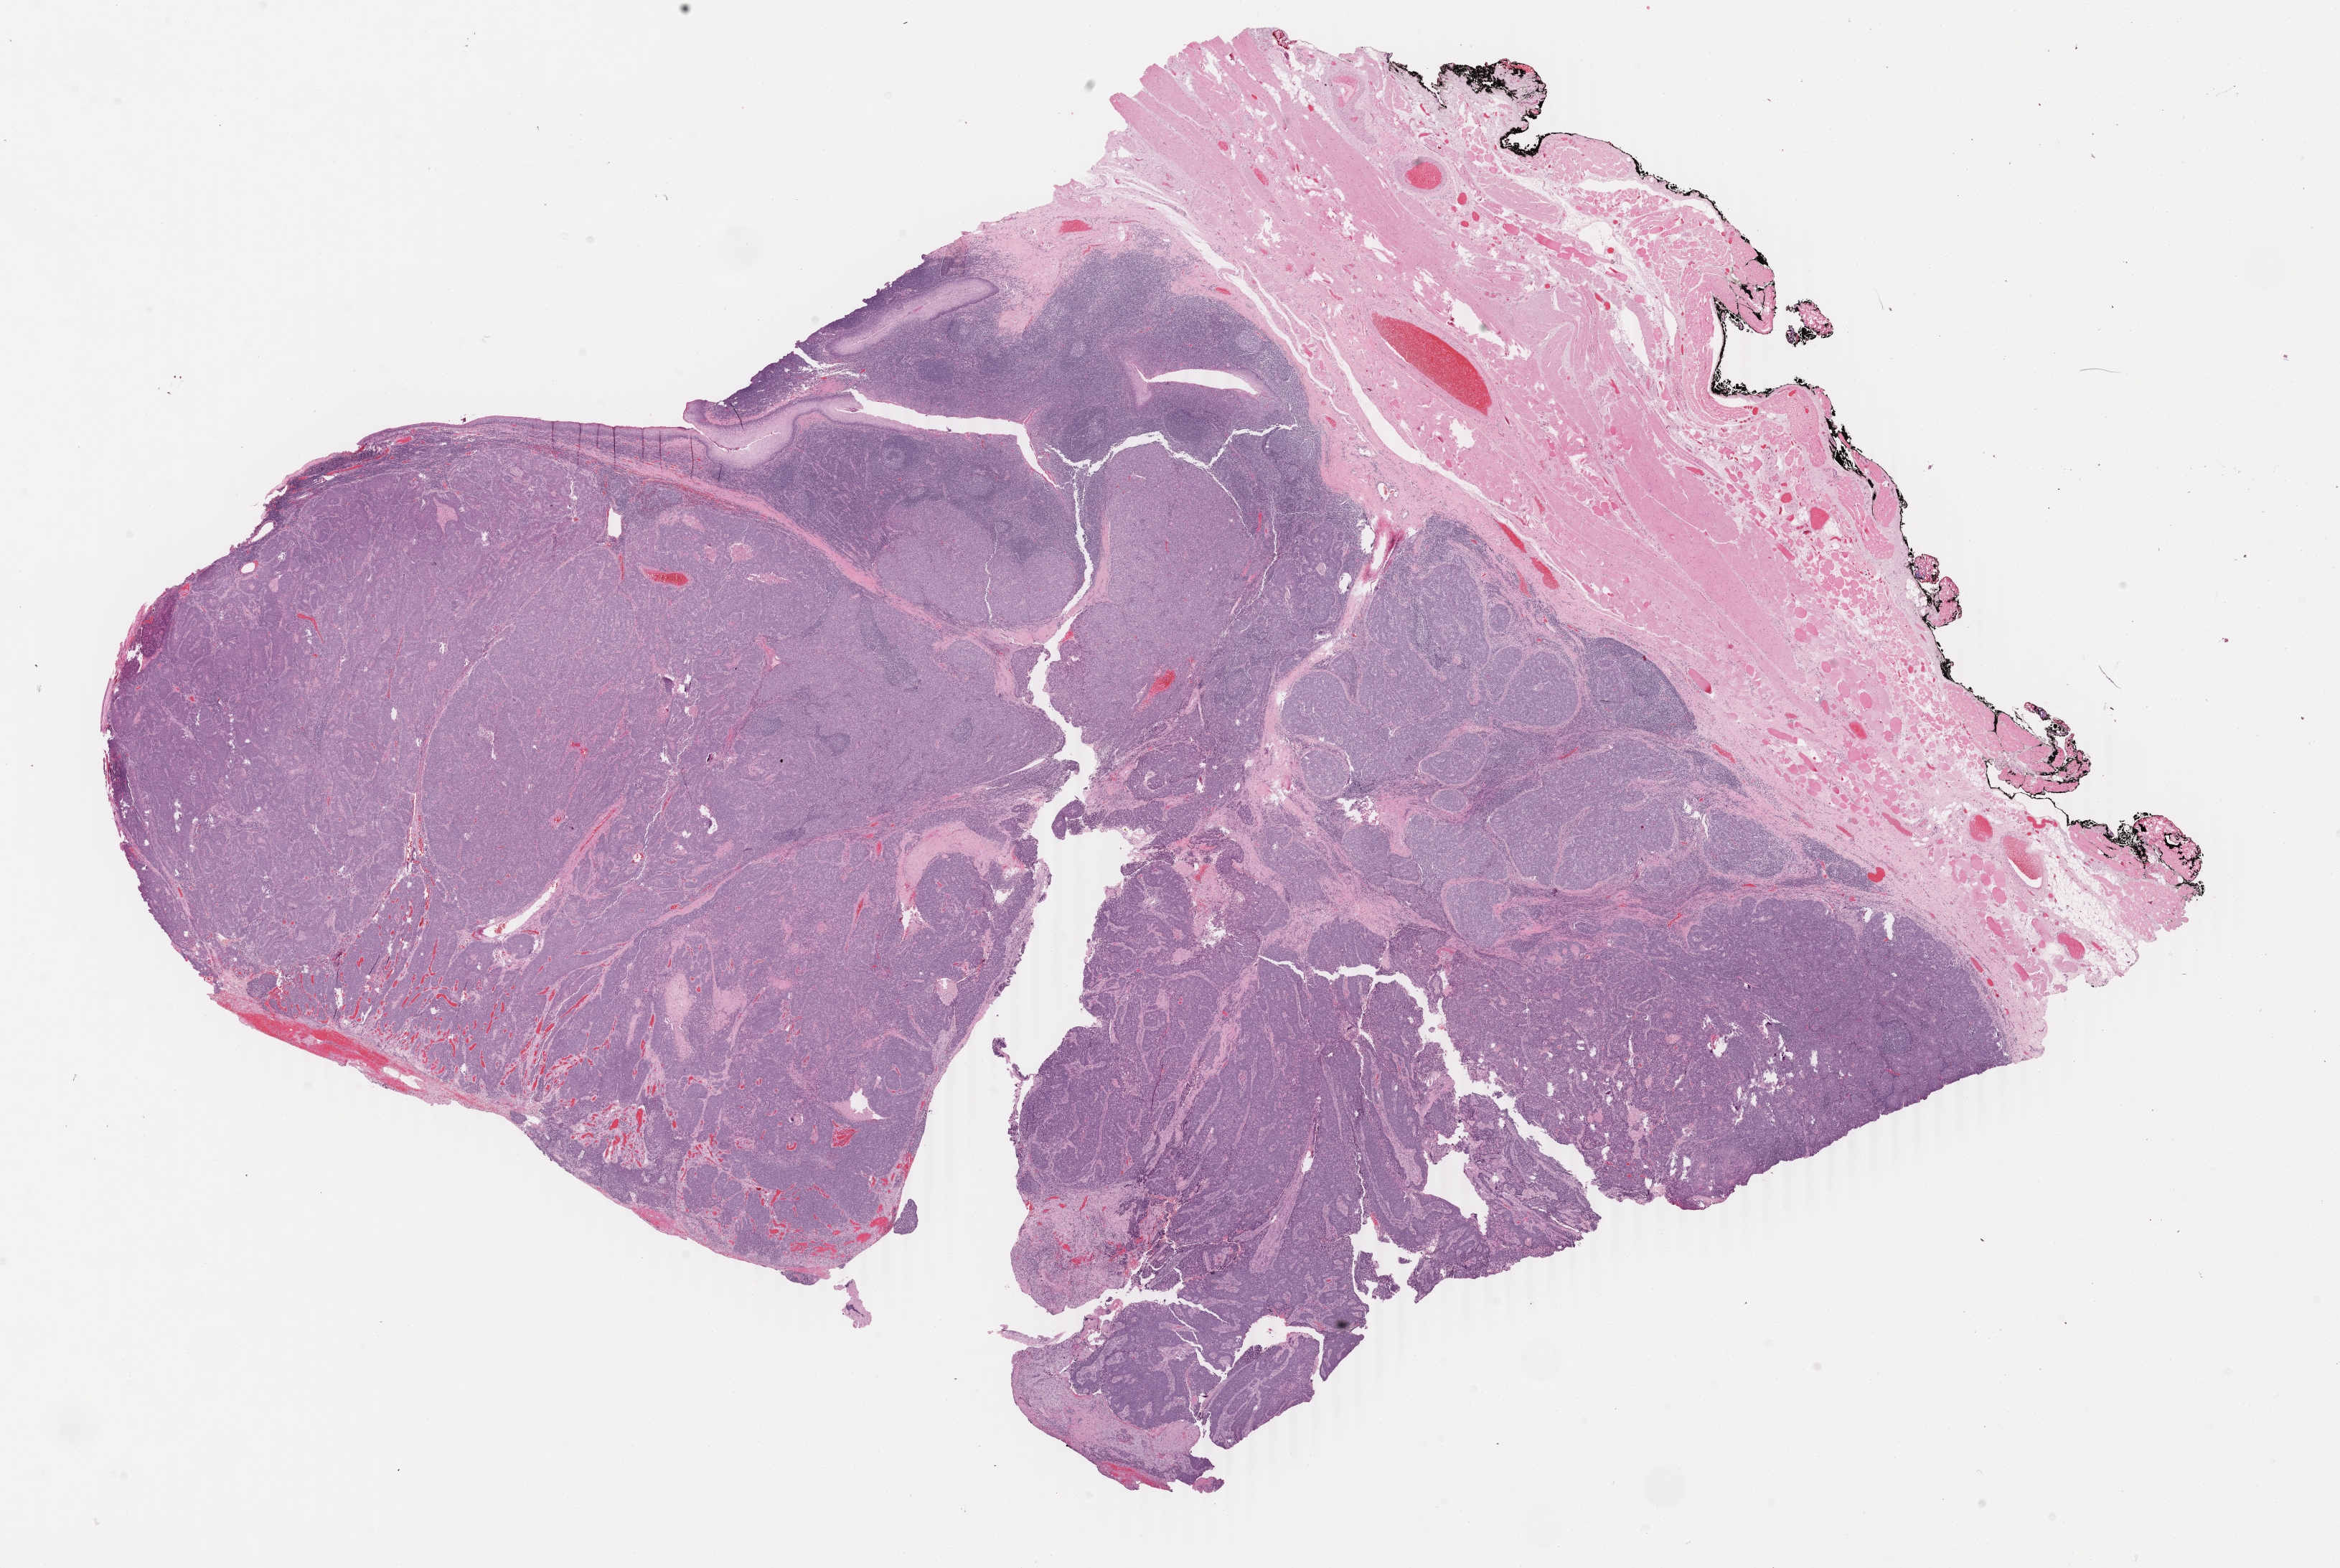
H&E whole-slide image — whole scanned area (about 25.9 x 17.4 mm, acquisition: 40x scan) shown as a low-resolution overview; formalin-fixed paraffin-embedded (FFPE) diagnostic section; primary tumour sample from the head and neck. Patient: male, age at initial diagnosis 63 years. Histologic grade: G3 (poorly differentiated).
AJCC pathologic stage: IVA. Lymph nodes positive (case pathology): 3 of 41 examined. Diagnosis: Squamous cell carcinoma, large cell, nonkeratinizing, NOS (tonsil, NOS).